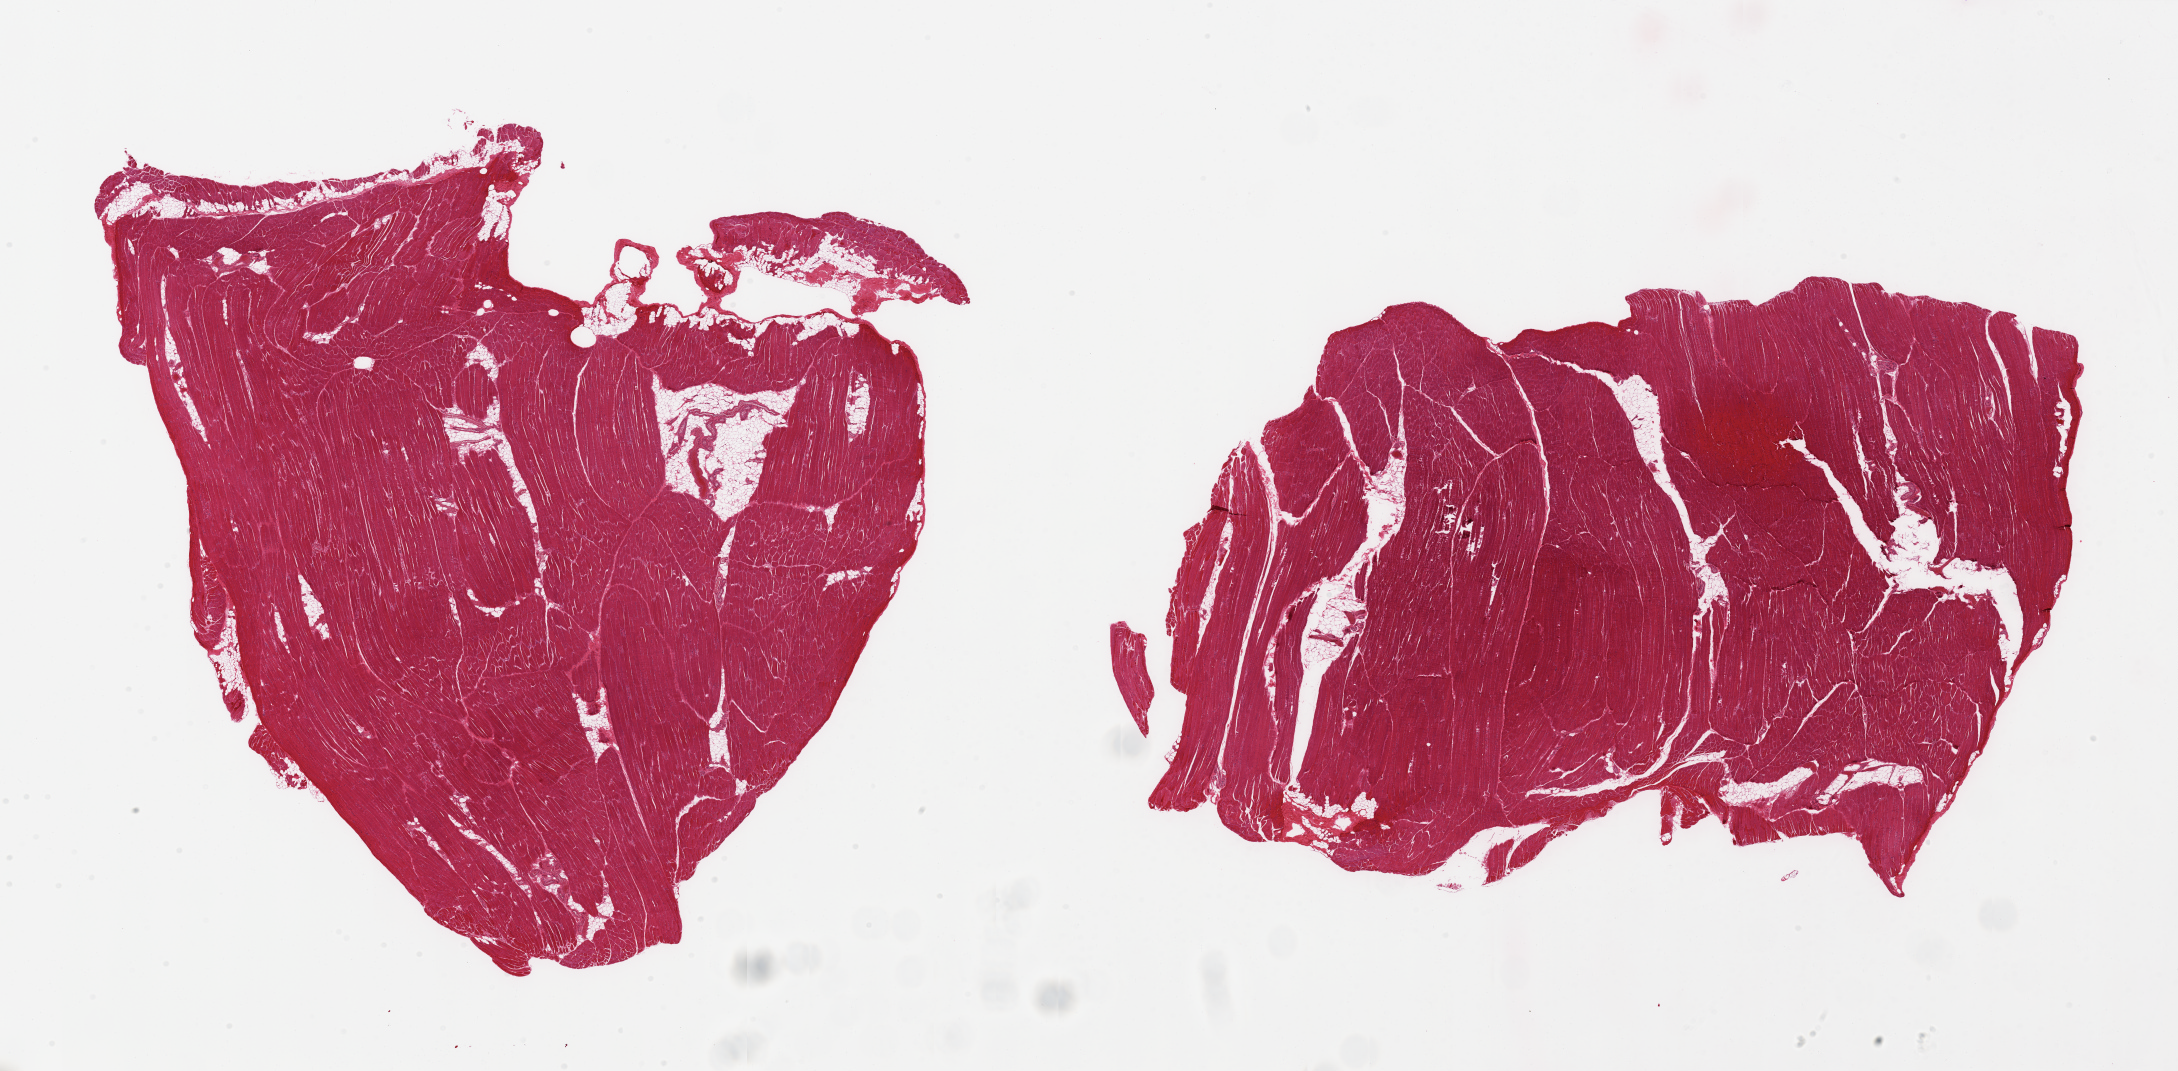
Haematoxylin and eosin whole-slide image — shown as a low-resolution overview of the whole scanned area (about 34.5 x 16.9 mm, slide scanned at 20x); PAXgene-fixed, paraffin-embedded tissue; section of skeletal muscle (target tissue); donor tissue sample. Donor: male.
- pathologist's review note for this sample: 2 pieces, interstitial fat 10-15%